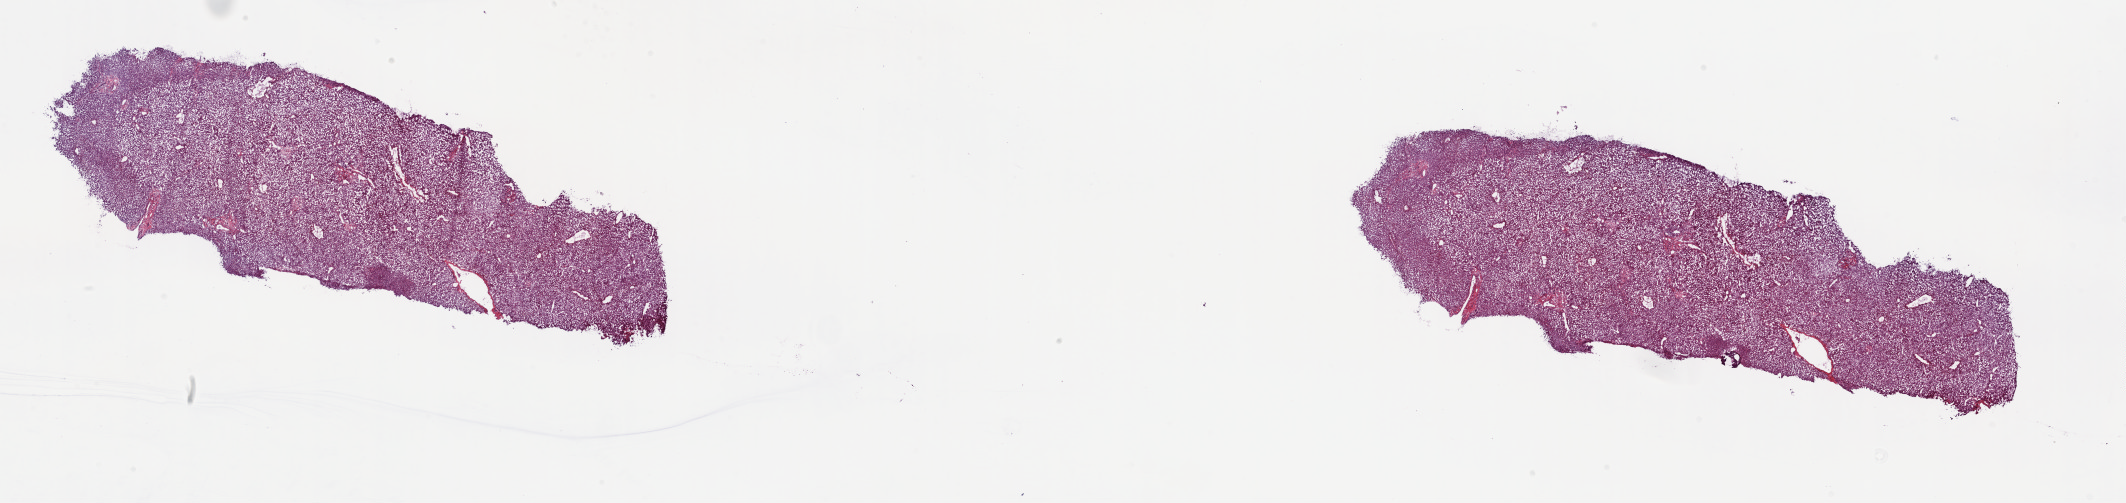
H&E whole-slide image, a low-resolution overview of the entire scanned area, about 33.7 x 8.0 mm, frozen section from the top of the tissue portion, sample: solid tissue normal (non-tumour tissue), bile duct. Female, age 64 years at initial diagnosis. Pathologist review of this section (percent, as recorded): tumour cells 0%, tumour nuclei 0%, normal cells 100%, stromal cells 0%, necrosis 0%. Infiltration values recorded for this section: lymphocyte infiltration 0%, monocyte infiltration 0%, neutrophil infiltration 0%.
- this section: solid tissue normal sample (biorepository sample class)
- patient diagnosis: Cholangiocarcinoma (intrahepatic bile duct)